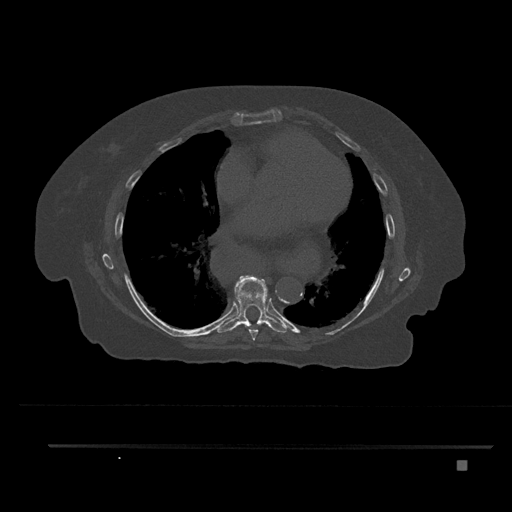
CT including the spine, one axial slice. Slice 458 of 797 in the series (ordered by position). Reconstruction kernel Br40s/3. Bone window (W 1800 / L 400 HU). 512 × 512 image matrix, field of view 437 × 437 mm. Patient: female, 76 years. From the clinical record (not read from this slice): primary cancer: lung.
Annotated regions visible in this slice (semi-automatically segmented with operator editing):
- T7 vertebra: bounding box <248,327,259,341> (left, top, right, bottom; pixels)
- T8 vertebra: <217,276,287,333>